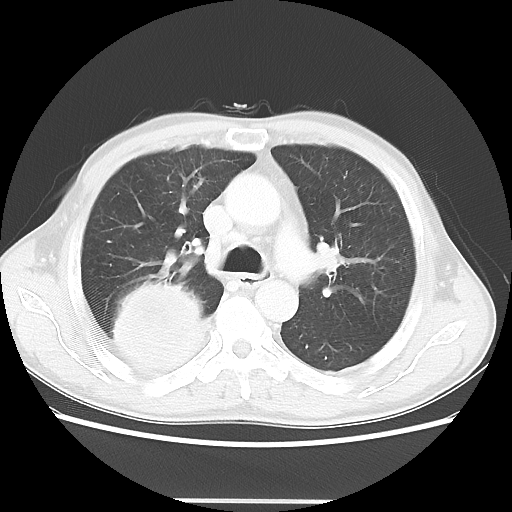
Chest CT, one axial slice. Position 33 of 48 along the scan axis. Reconstruction kernel LUNG. 100 kVp. Lung window (W 1500 / L -600 HU). 512 × 512 image matrix. Patient: male, 66 years. Case-level facts recorded for this patient, not image findings: clinical TNM (as recorded): T4 N1 M1; histopathological grade: G3.
Annotated regions visible in this slice (bounding box drawn by a radiologist):
- lung tumour (recorded histology: small cell carcinoma): bounding box [x1, y1, x2, y2] px = [100, 270, 207, 375]